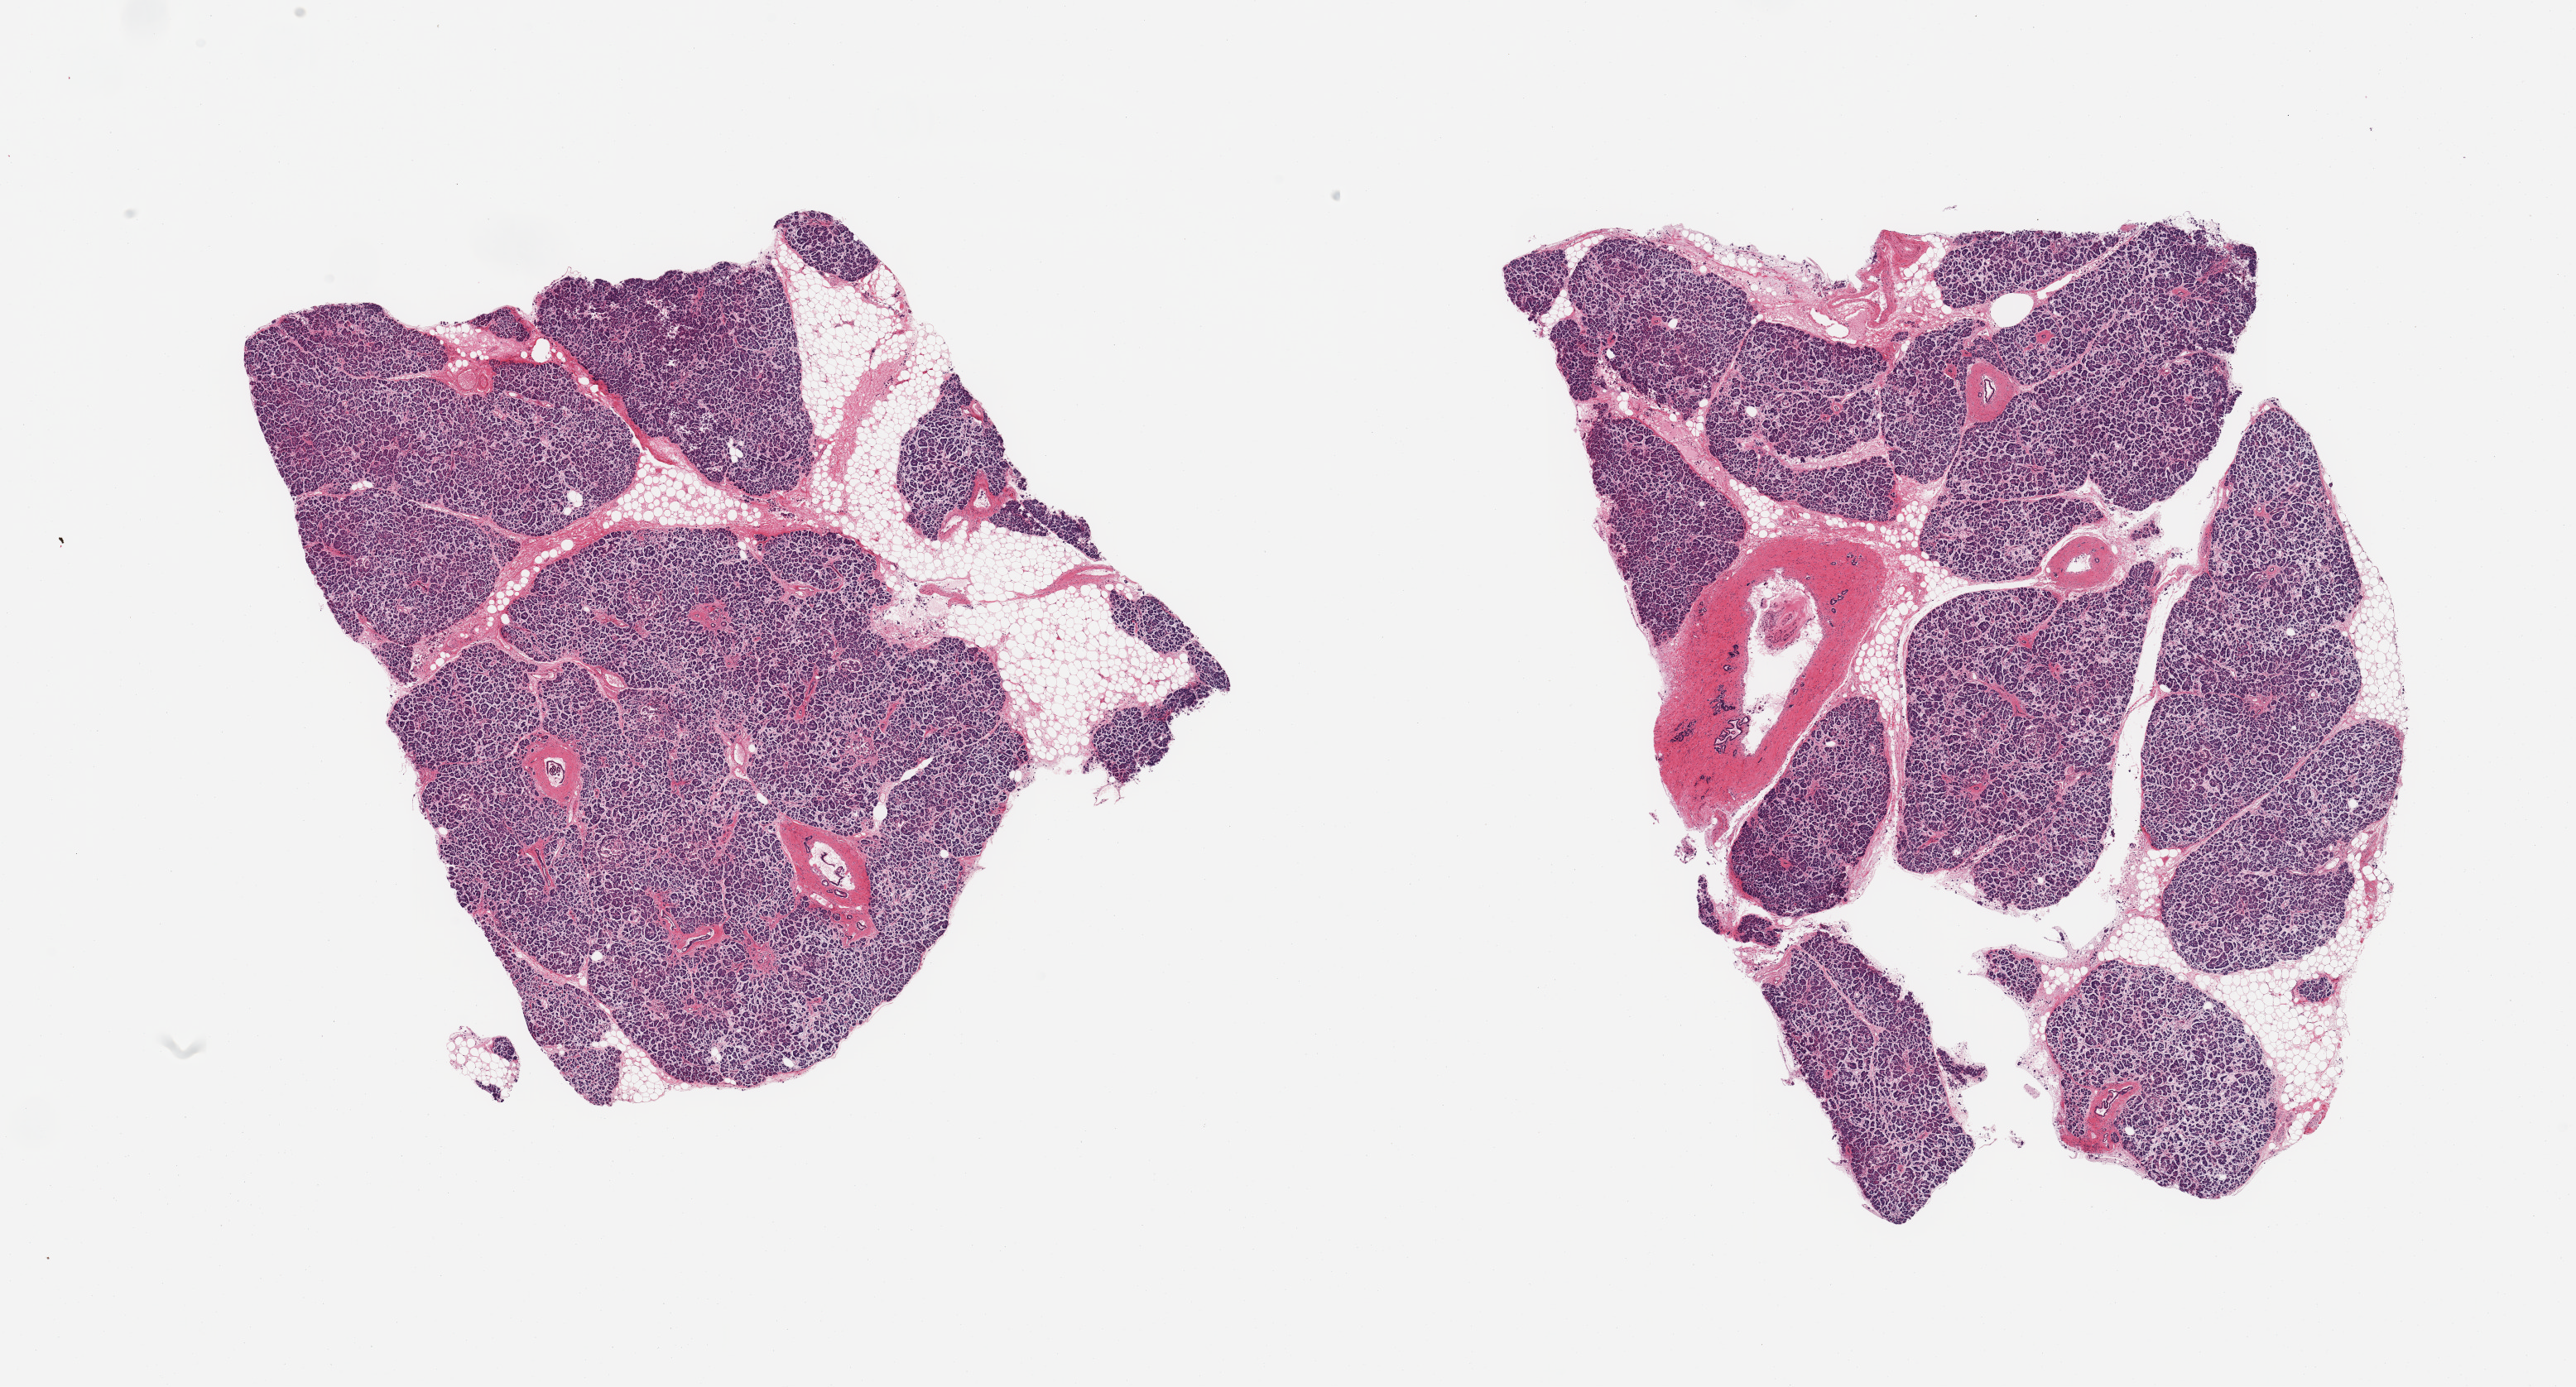
Digitized hematoxylin and eosin (H&E)-stained section, whole scanned area (about 24.6 x 13.3 mm, slide scanned at 20x) shown as a low-resolution overview; PAXgene-fixed, paraffin-embedded tissue; target tissue: pancreas; tissue donor sample. Donor sex: male.
* review note (as recorded): 2 pieces, saponification moderately advanced; an occasional islet visible but largely degenerated